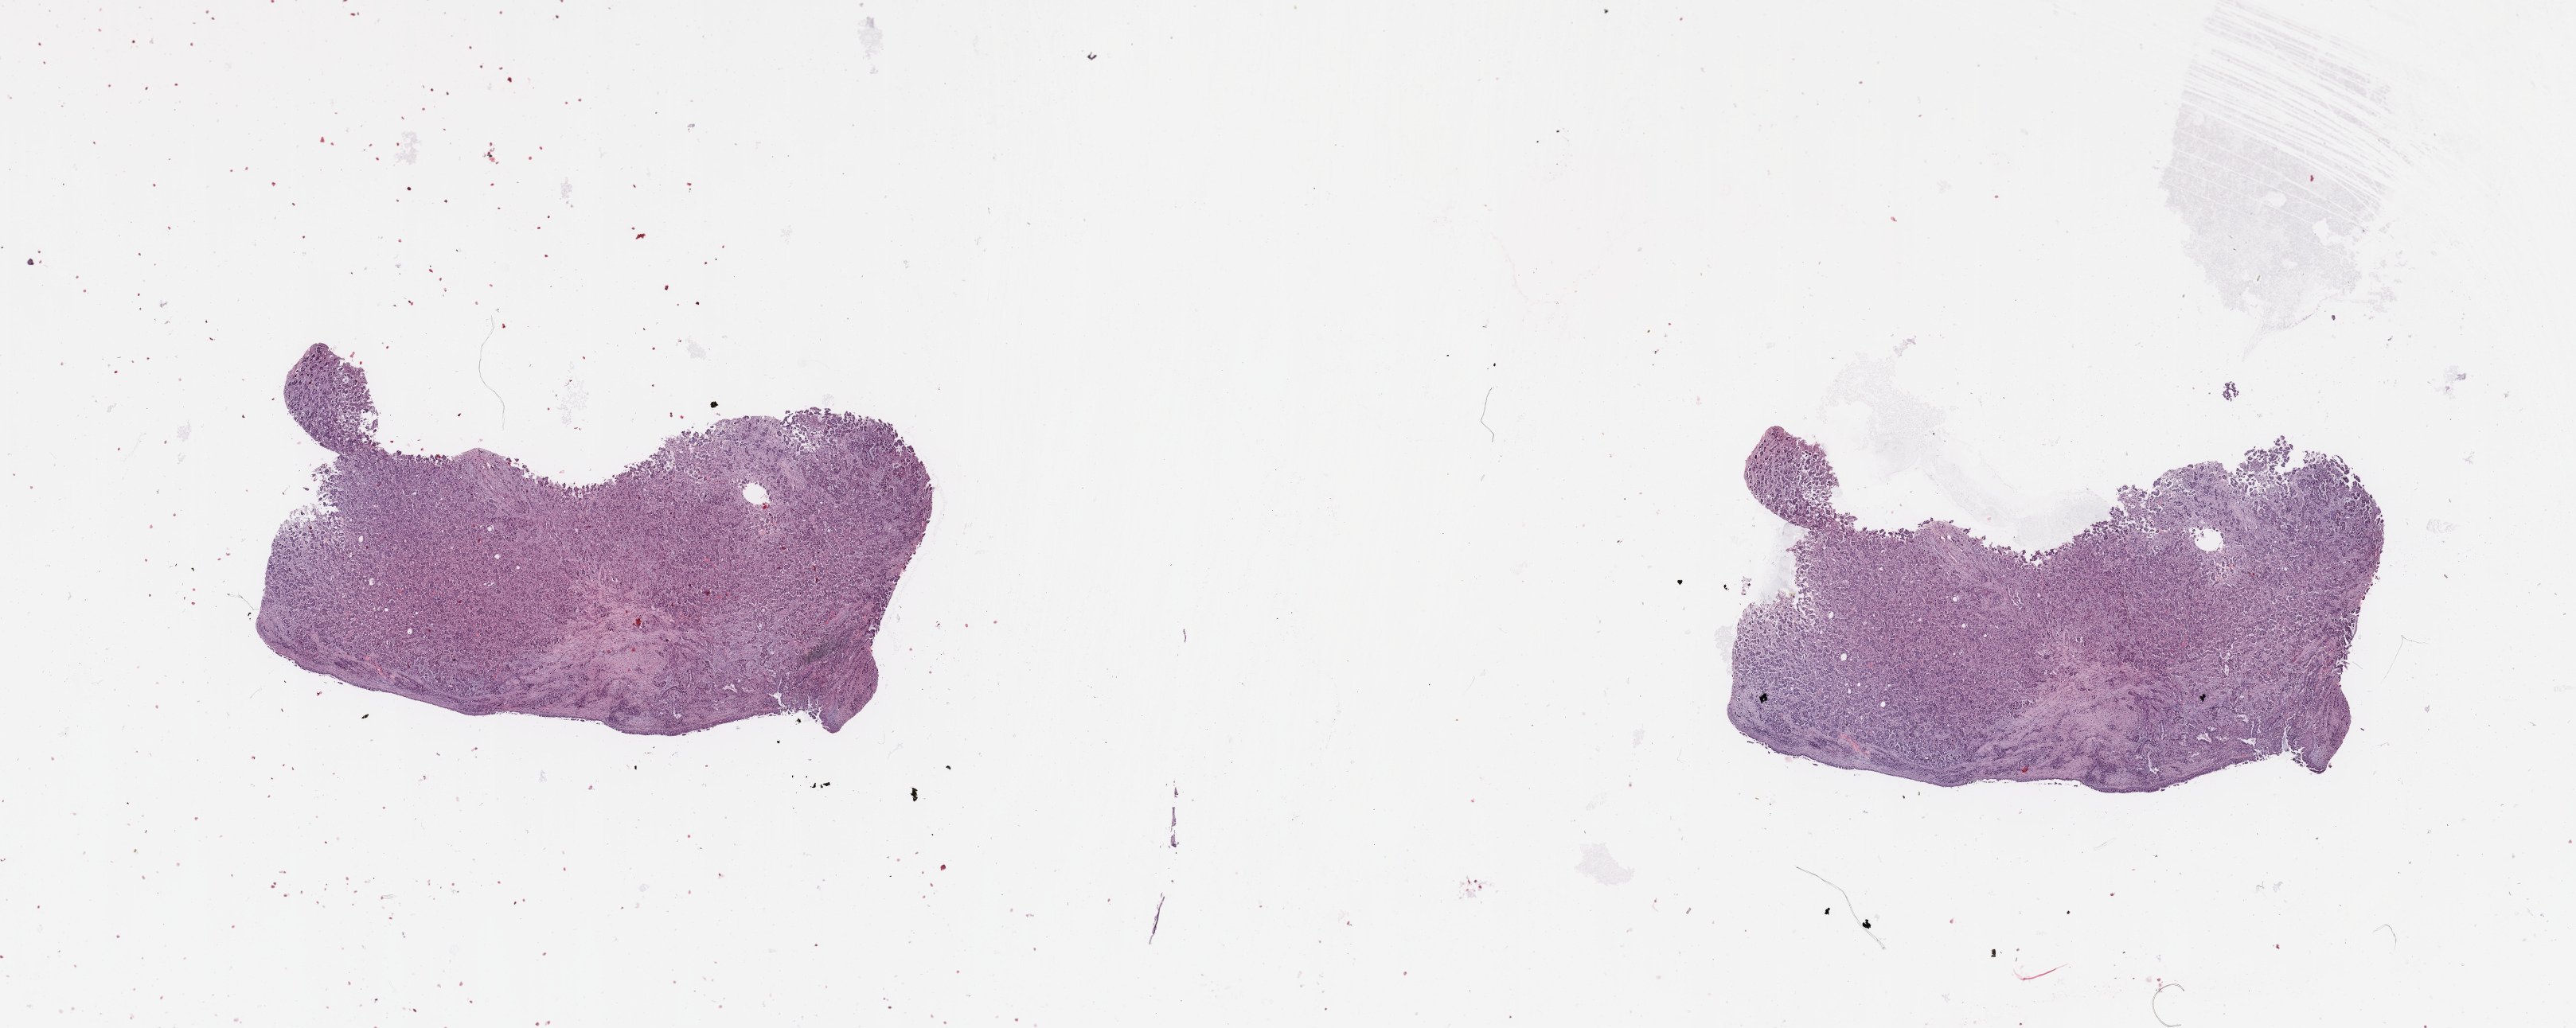
Whole-slide histology image, H&E, shown as a low-resolution overview of the whole scanned area (about 25.6 x 10.2 mm, slide scanned at 20x); lung, tumour tissue. Patient: male, age 39 years. Histologic grade: G2 (moderately differentiated).
Histologic diagnosis: Adenocarcinoma, NOS. AJCC pathologic stage: IIIA.